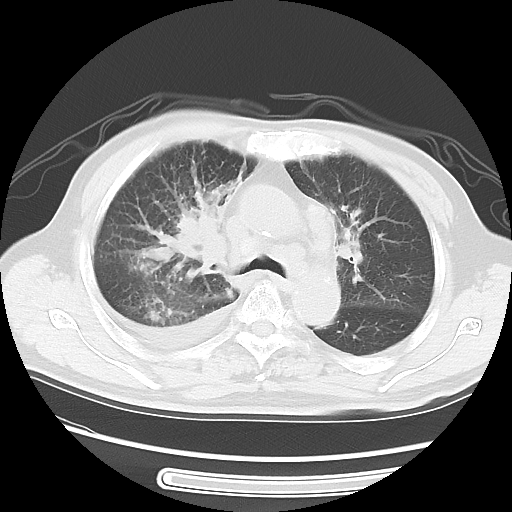
Chest CT, one axial slice; position 37 of 56 along the scan axis; reconstruction kernel LUNG; lung window (W 1500 / L -600 HU); 5 mm slice thickness; 512 × 512 image matrix, field of view 360 × 360 mm. Patient: male, 77 years. From the clinical record (not read from this slice): clinical TNM (as recorded): T3 N3 M1b.
Outlined on this slice (rectangle marked by the reading radiologist):
- lung tumour (recorded histology: small cell carcinoma): box from (x=163, y=198) to (x=235, y=284) px